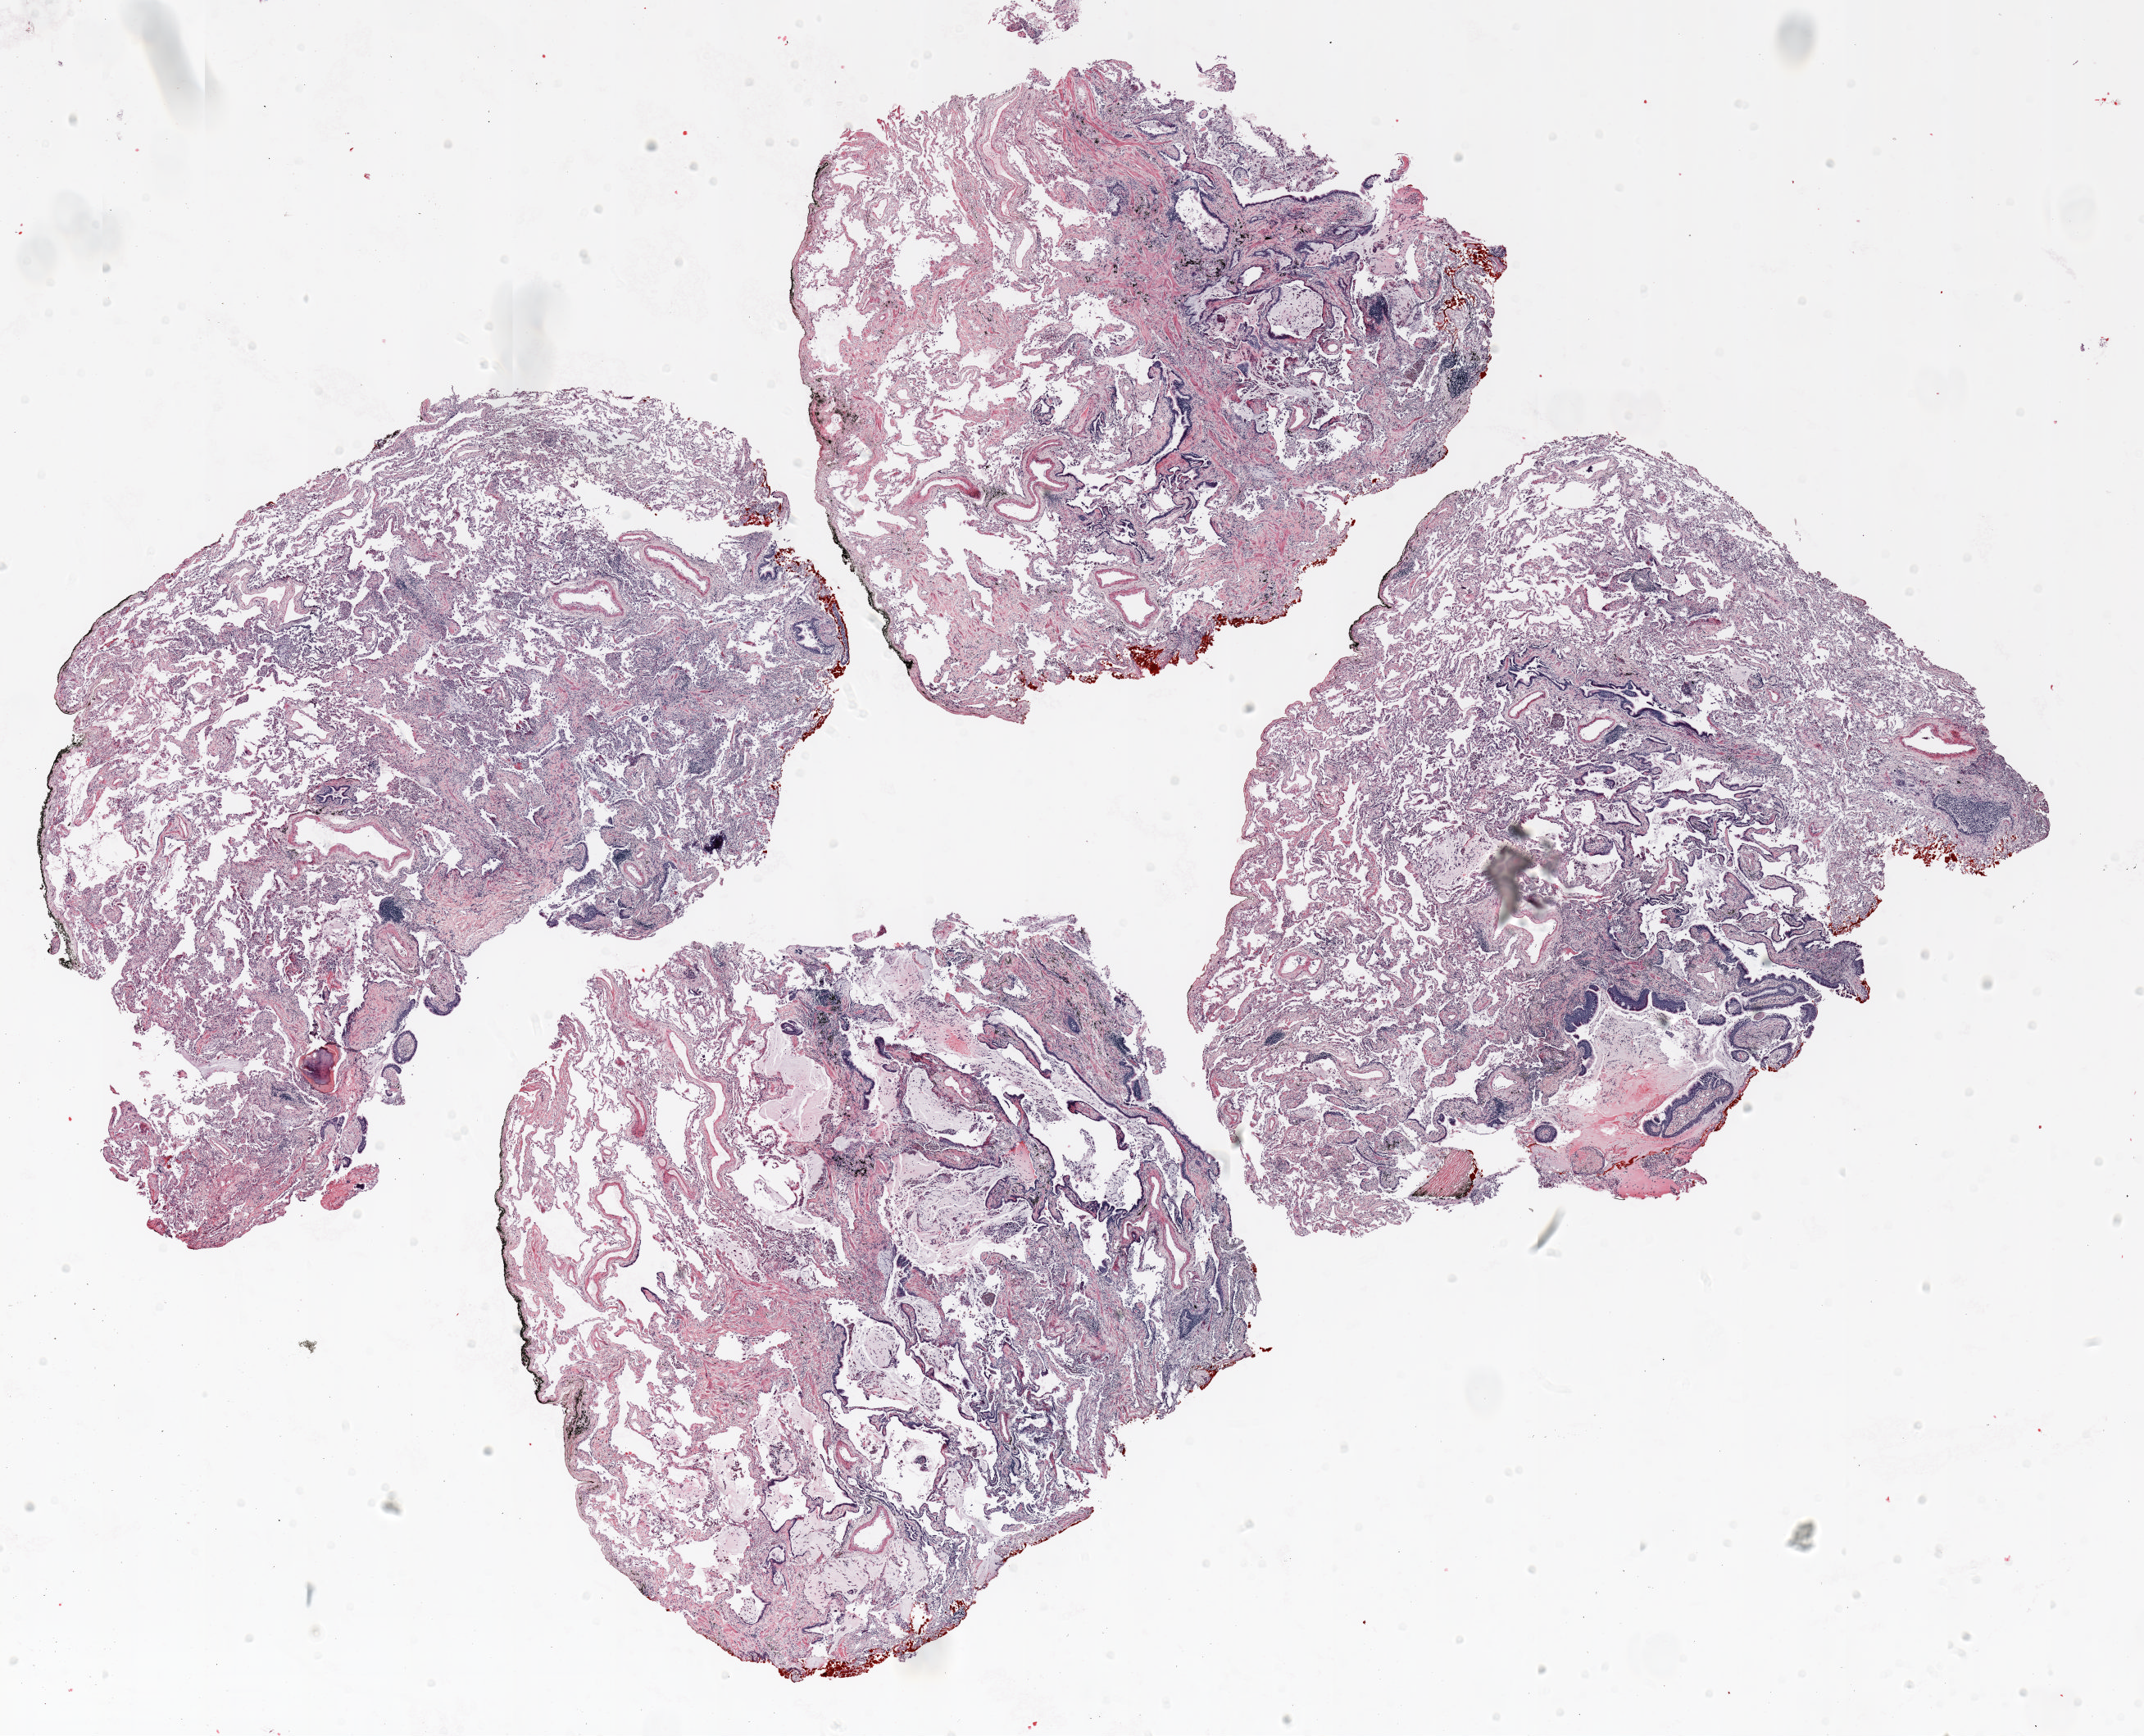
H&E whole-slide image, a low-resolution overview of the entire scanned area, about 21.0 x 17.0 mm (acquisition: 20x scan), formalin-fixed paraffin-embedded (FFPE) section, lung tissue. Male, age 67 at enrolment. Former smoker at enrolment.
Participant's lung-cancer diagnosis: Squamous cell carcinoma, NOS (ICD-O-3 8070/3).